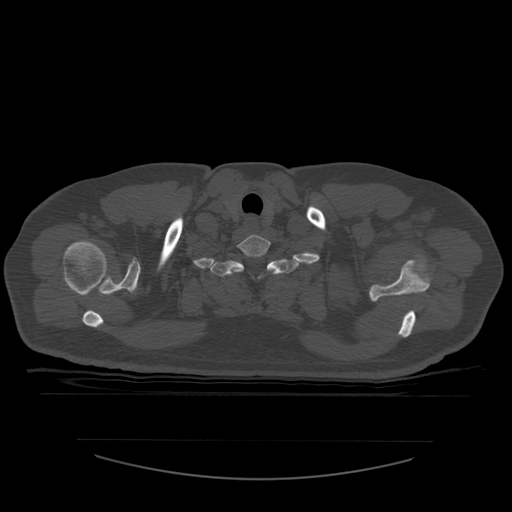
CT including the spine, one axial slice; position 473 of 532 along the scan axis; reconstruction kernel STANDARD; bone window (W 1800 / L 400 HU); 1.25 mm slice thickness; 512 × 512 image matrix. Patient age 44 years. From the clinical record (not read from this slice): primary cancer: soft tissue sarcoma.
Structures marked on this image (semi-automatically segmented with operator editing):
- T1 vertebra: bounding box [x1, y1, x2, y2] px = [211, 258, 301, 279]